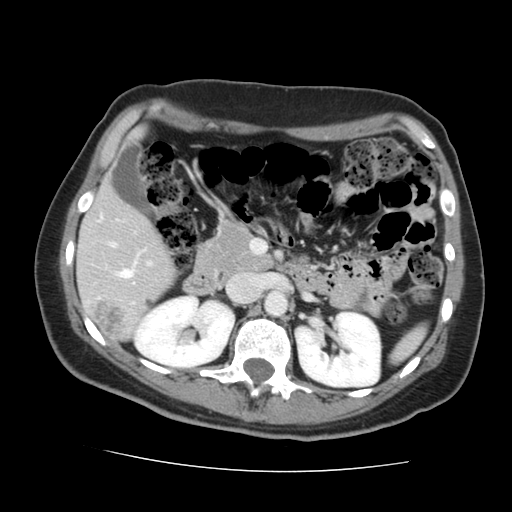
Contrast-enhanced abdominal CT, one axial slice. Slice 75 of 144 in the series (ordered by position). Soft-tissue window (W 400 / L 40 HU). 512 × 512 image matrix. Female patient, age 46 years. Case-level facts recorded for this patient, not image findings: diagnosis: colorectal cancer liver metastases, imaged before liver resection.
Outlined on this slice (outlined manually by an expert reader):
- liver: bounding box [x1, y1, x2, y2] px = [78, 186, 177, 340]
- planned liver remnant (the part of the liver to remain after resection): [78, 186, 177, 338]
- portal vein (with intrahepatic branches): [101, 217, 151, 278]
- liver metastasis: [95, 302, 121, 336]